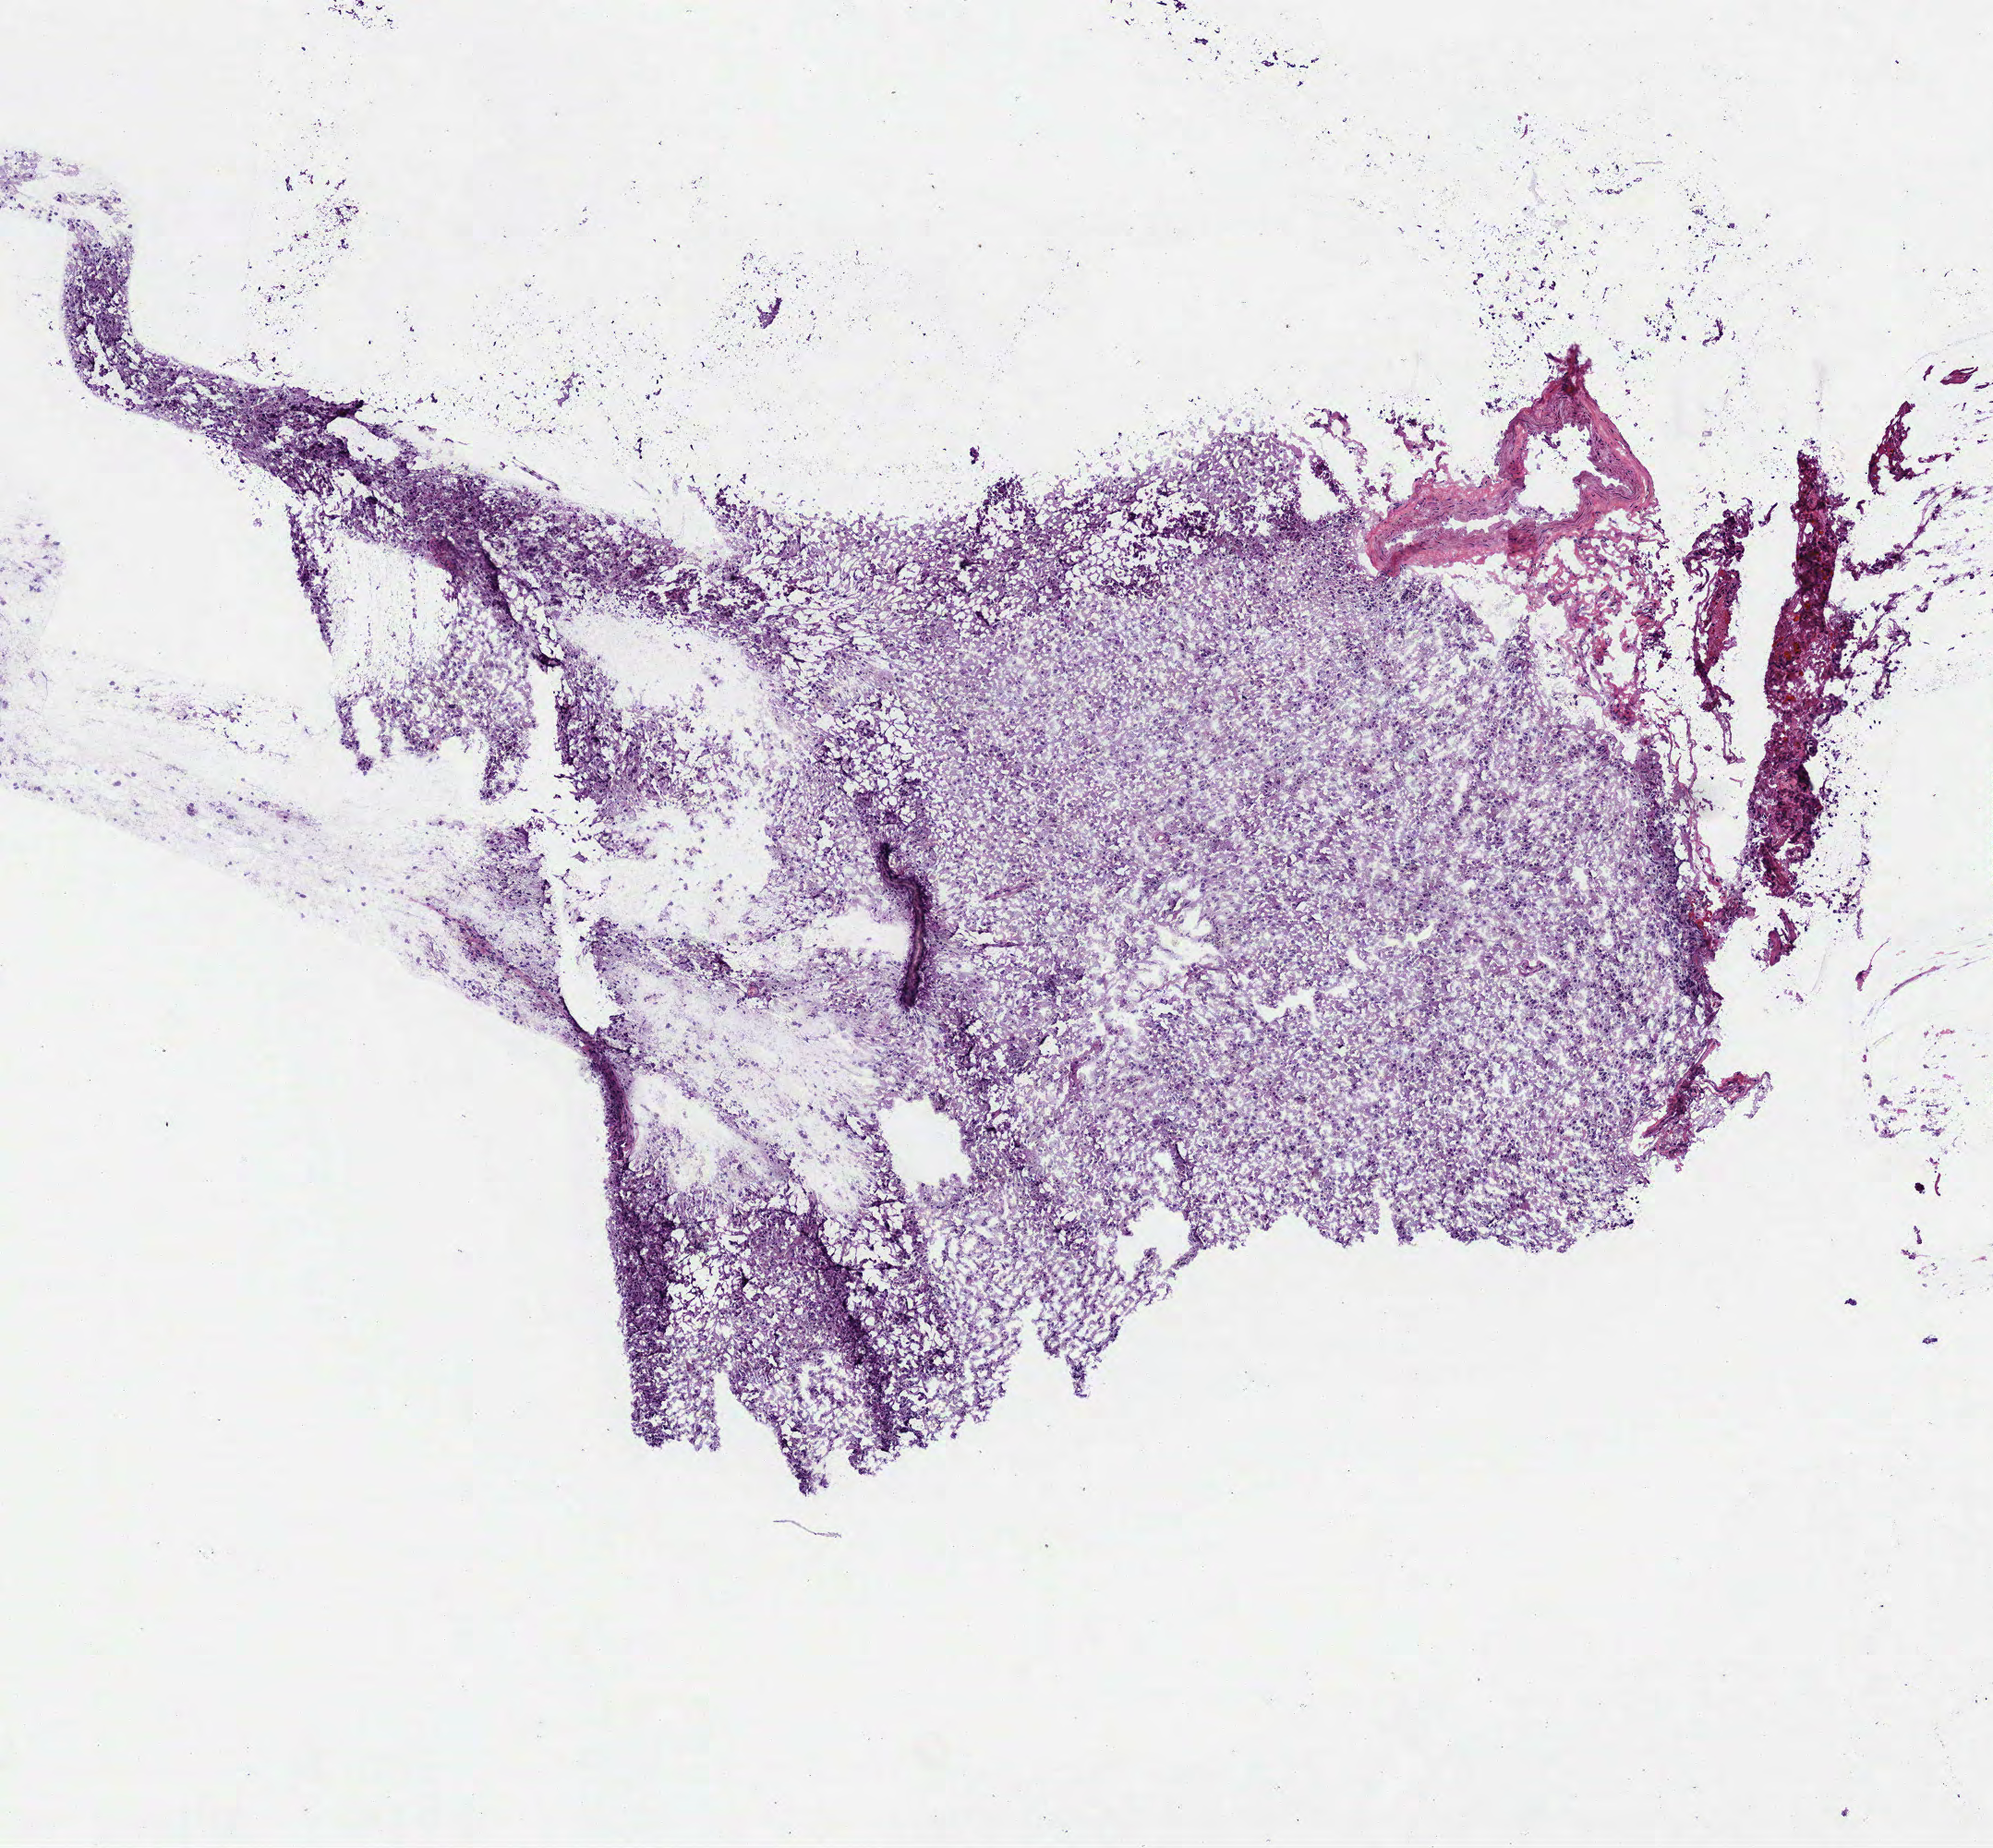
Whole-slide histology image, H&E-stained, low-resolution overview of the scanned area, about 4.4 x 4.0 mm (acquisition: 40x scan). Frozen section from the top of the tissue portion. Primary tumour sample from the brain. Patient: male, age at initial diagnosis 56 years. Histologic grade: G2 (moderately differentiated). Pathologist review of this section (percent, as recorded): tumour cells 100%, tumour nuclei 75%, normal cells 0%, stromal cells 0%, necrosis 0%.
Diagnosis: Oligodendroglioma, NOS.